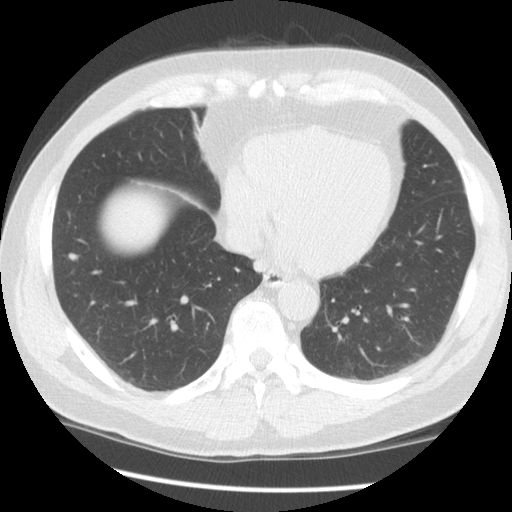
Low-dose screening chest CT, axial slice; second screening round (one year after baseline); lung window (W 1500 / L -600 HU); 2.5 mm slice thickness. Male participant, aged 61 years at enrolment. Current smoker at enrolment.
• Lesion marked by an expert reader, bounding box <51,244,86,278> (left, top, right, bottom; pixels).
• The exam's reader record, not a measurement of the box and not confirmed to be the same lesion: non-calcified nodule or mass ≥4 mm, right lower lobe, 5 × 4 mm, smooth margins, soft tissue attenuation, pre-existing on the prior screen: no.